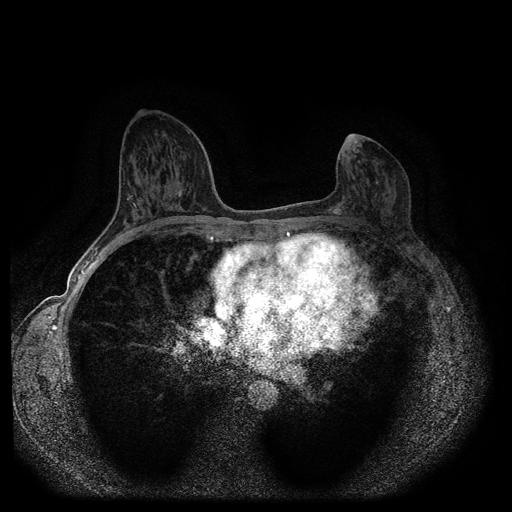
Breast MRI (dynamic contrast-enhanced, multi-phase), one axial slice. Position 50 of 116 along the scan axis. Dynamic contrast-enhanced series, time point 2 of 5 at this slice position (early post-contrast). 1.5 T. TE 2.6 ms, TR 5.4 ms. 2 mm slice thickness. 512 × 512 image matrix, field of view 340 × 340 mm. Patient: female, 57 years.
Structures marked on this image (semi-automatic segmentation, software-assisted and operator-edited):
- breast lesion (labelled 'tumour' in the annotation; benign lesions carry a separate 'benign' label): bounding box (x1, y1, x2, y2) in pixels: (328, 206, 343, 217)